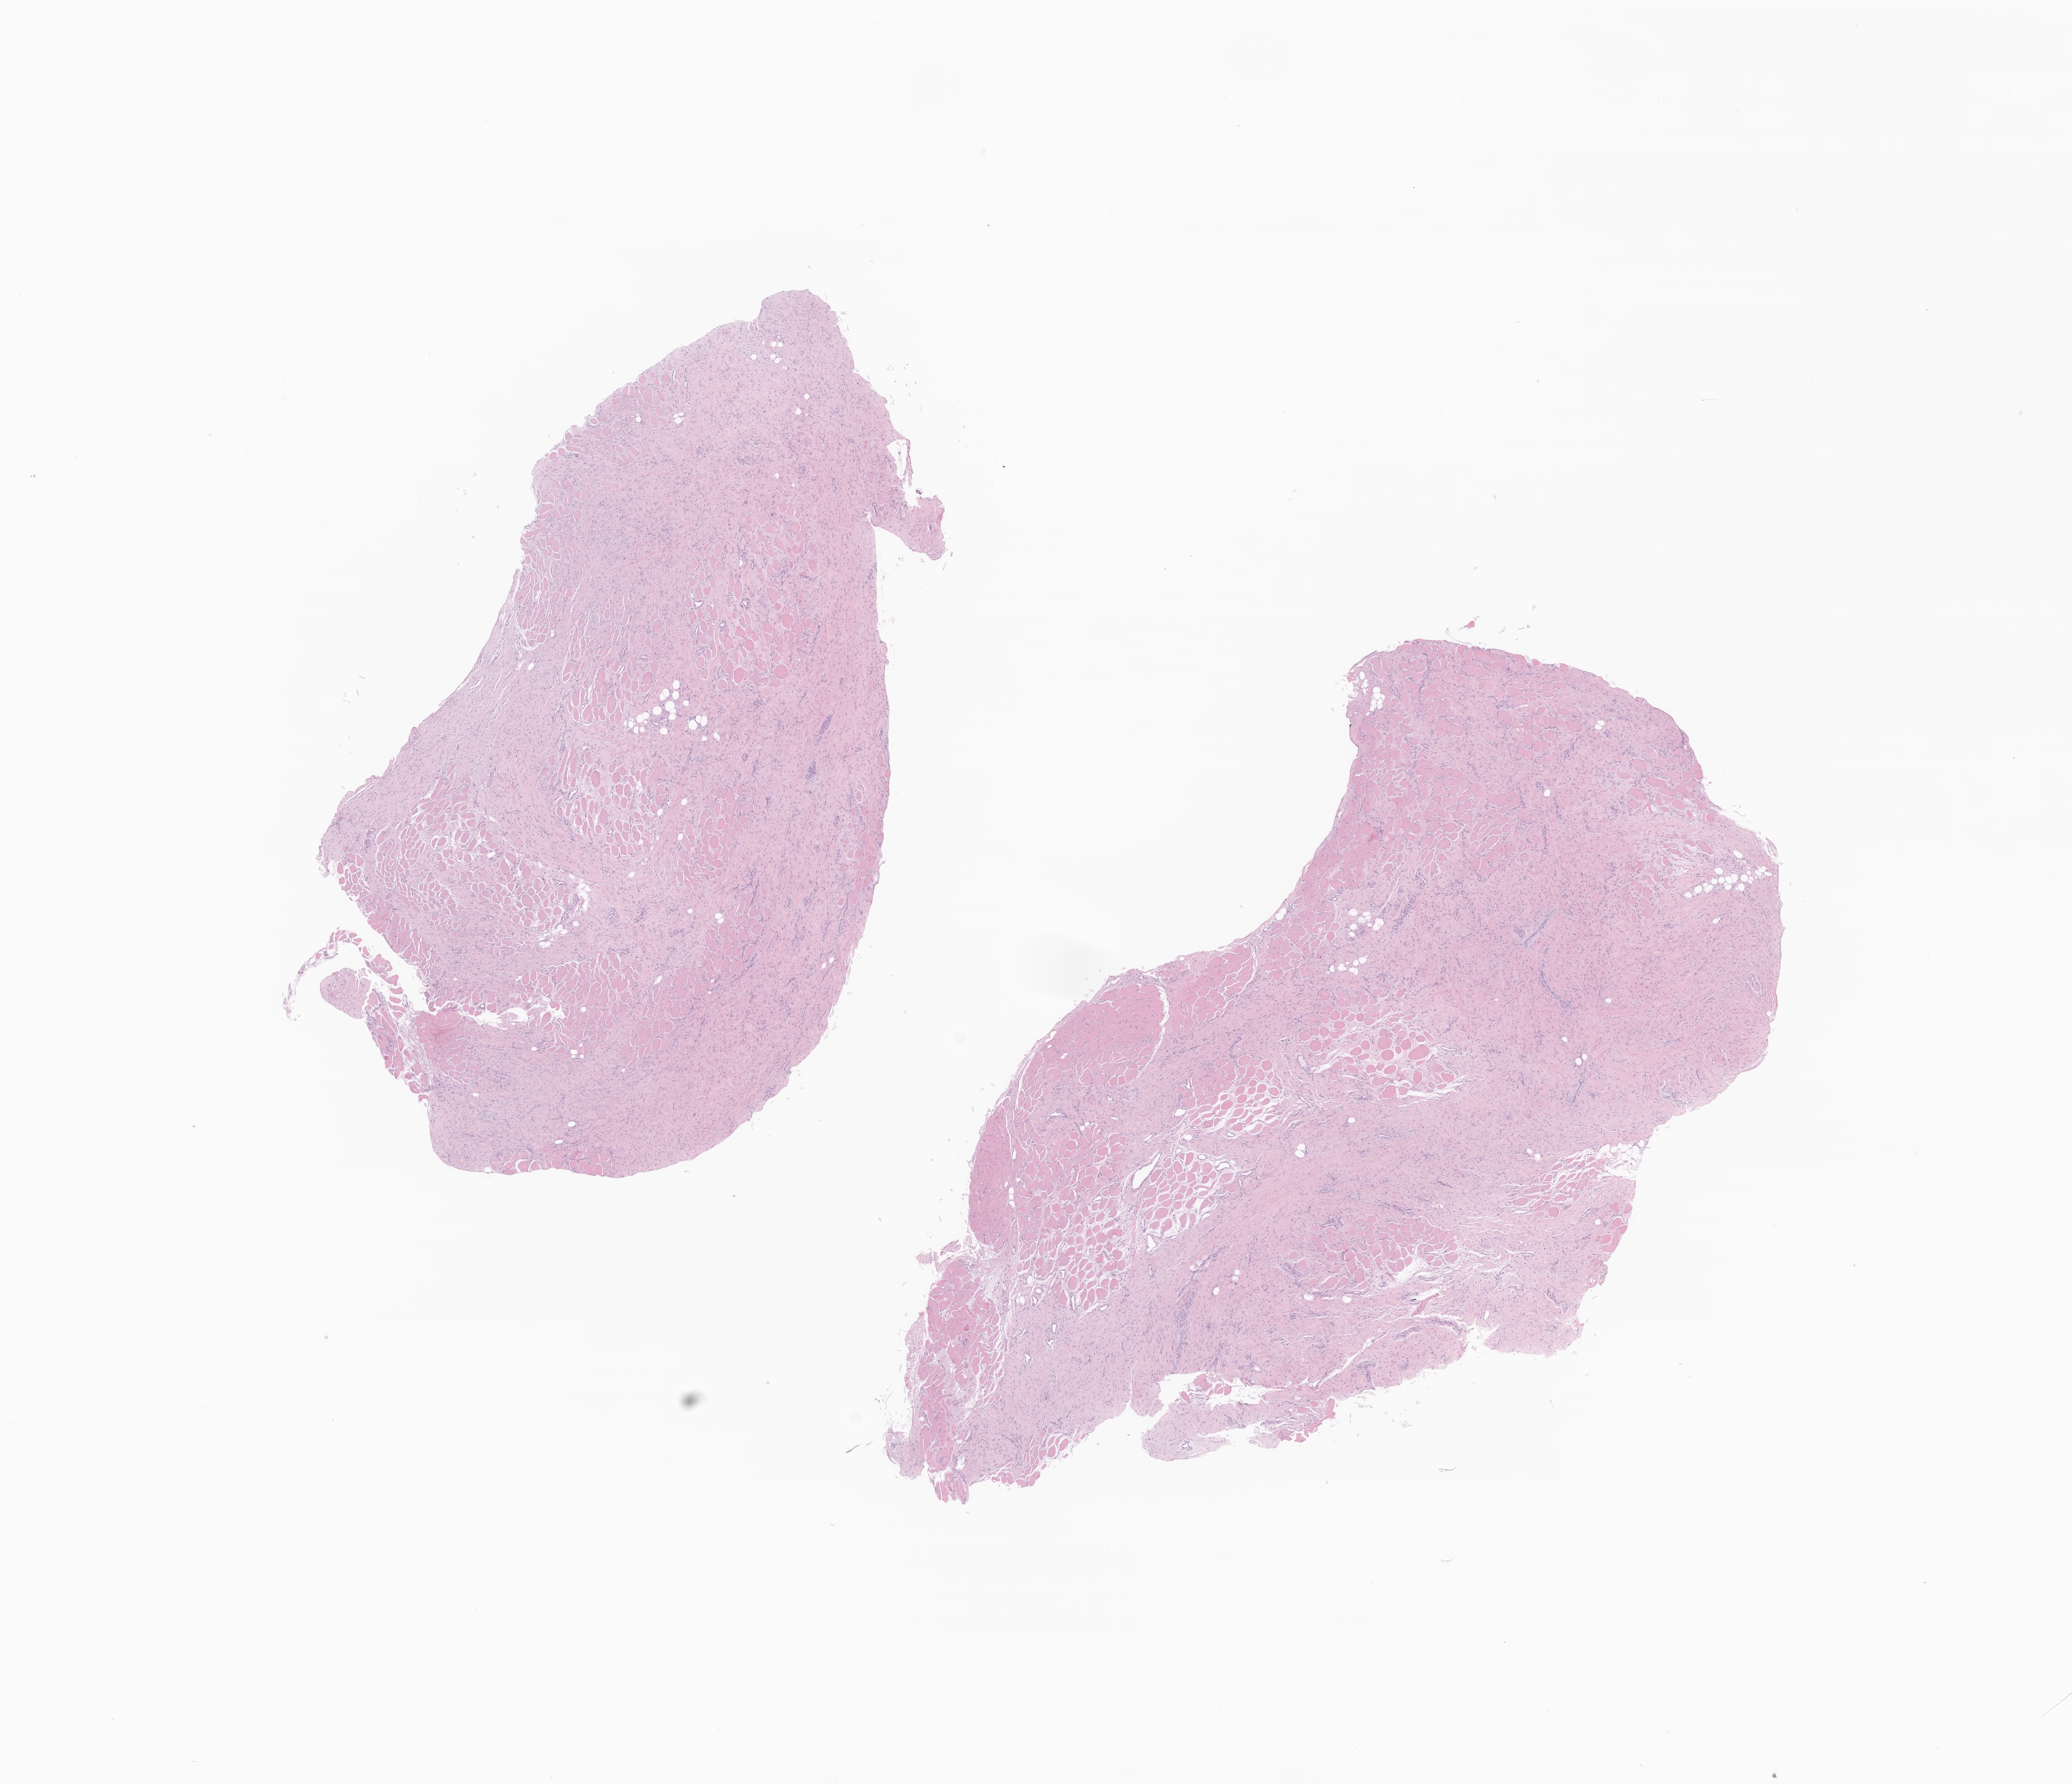
Haematoxylin and eosin whole-slide image of tumor tissue from the head and neck — a low-resolution overview of the entire scanned area, about 14.3 x 12.3 mm, FFPE section. Patient male; age 485 days (about 1.3 years).
Diagnosis: Sarcoma, NOS.